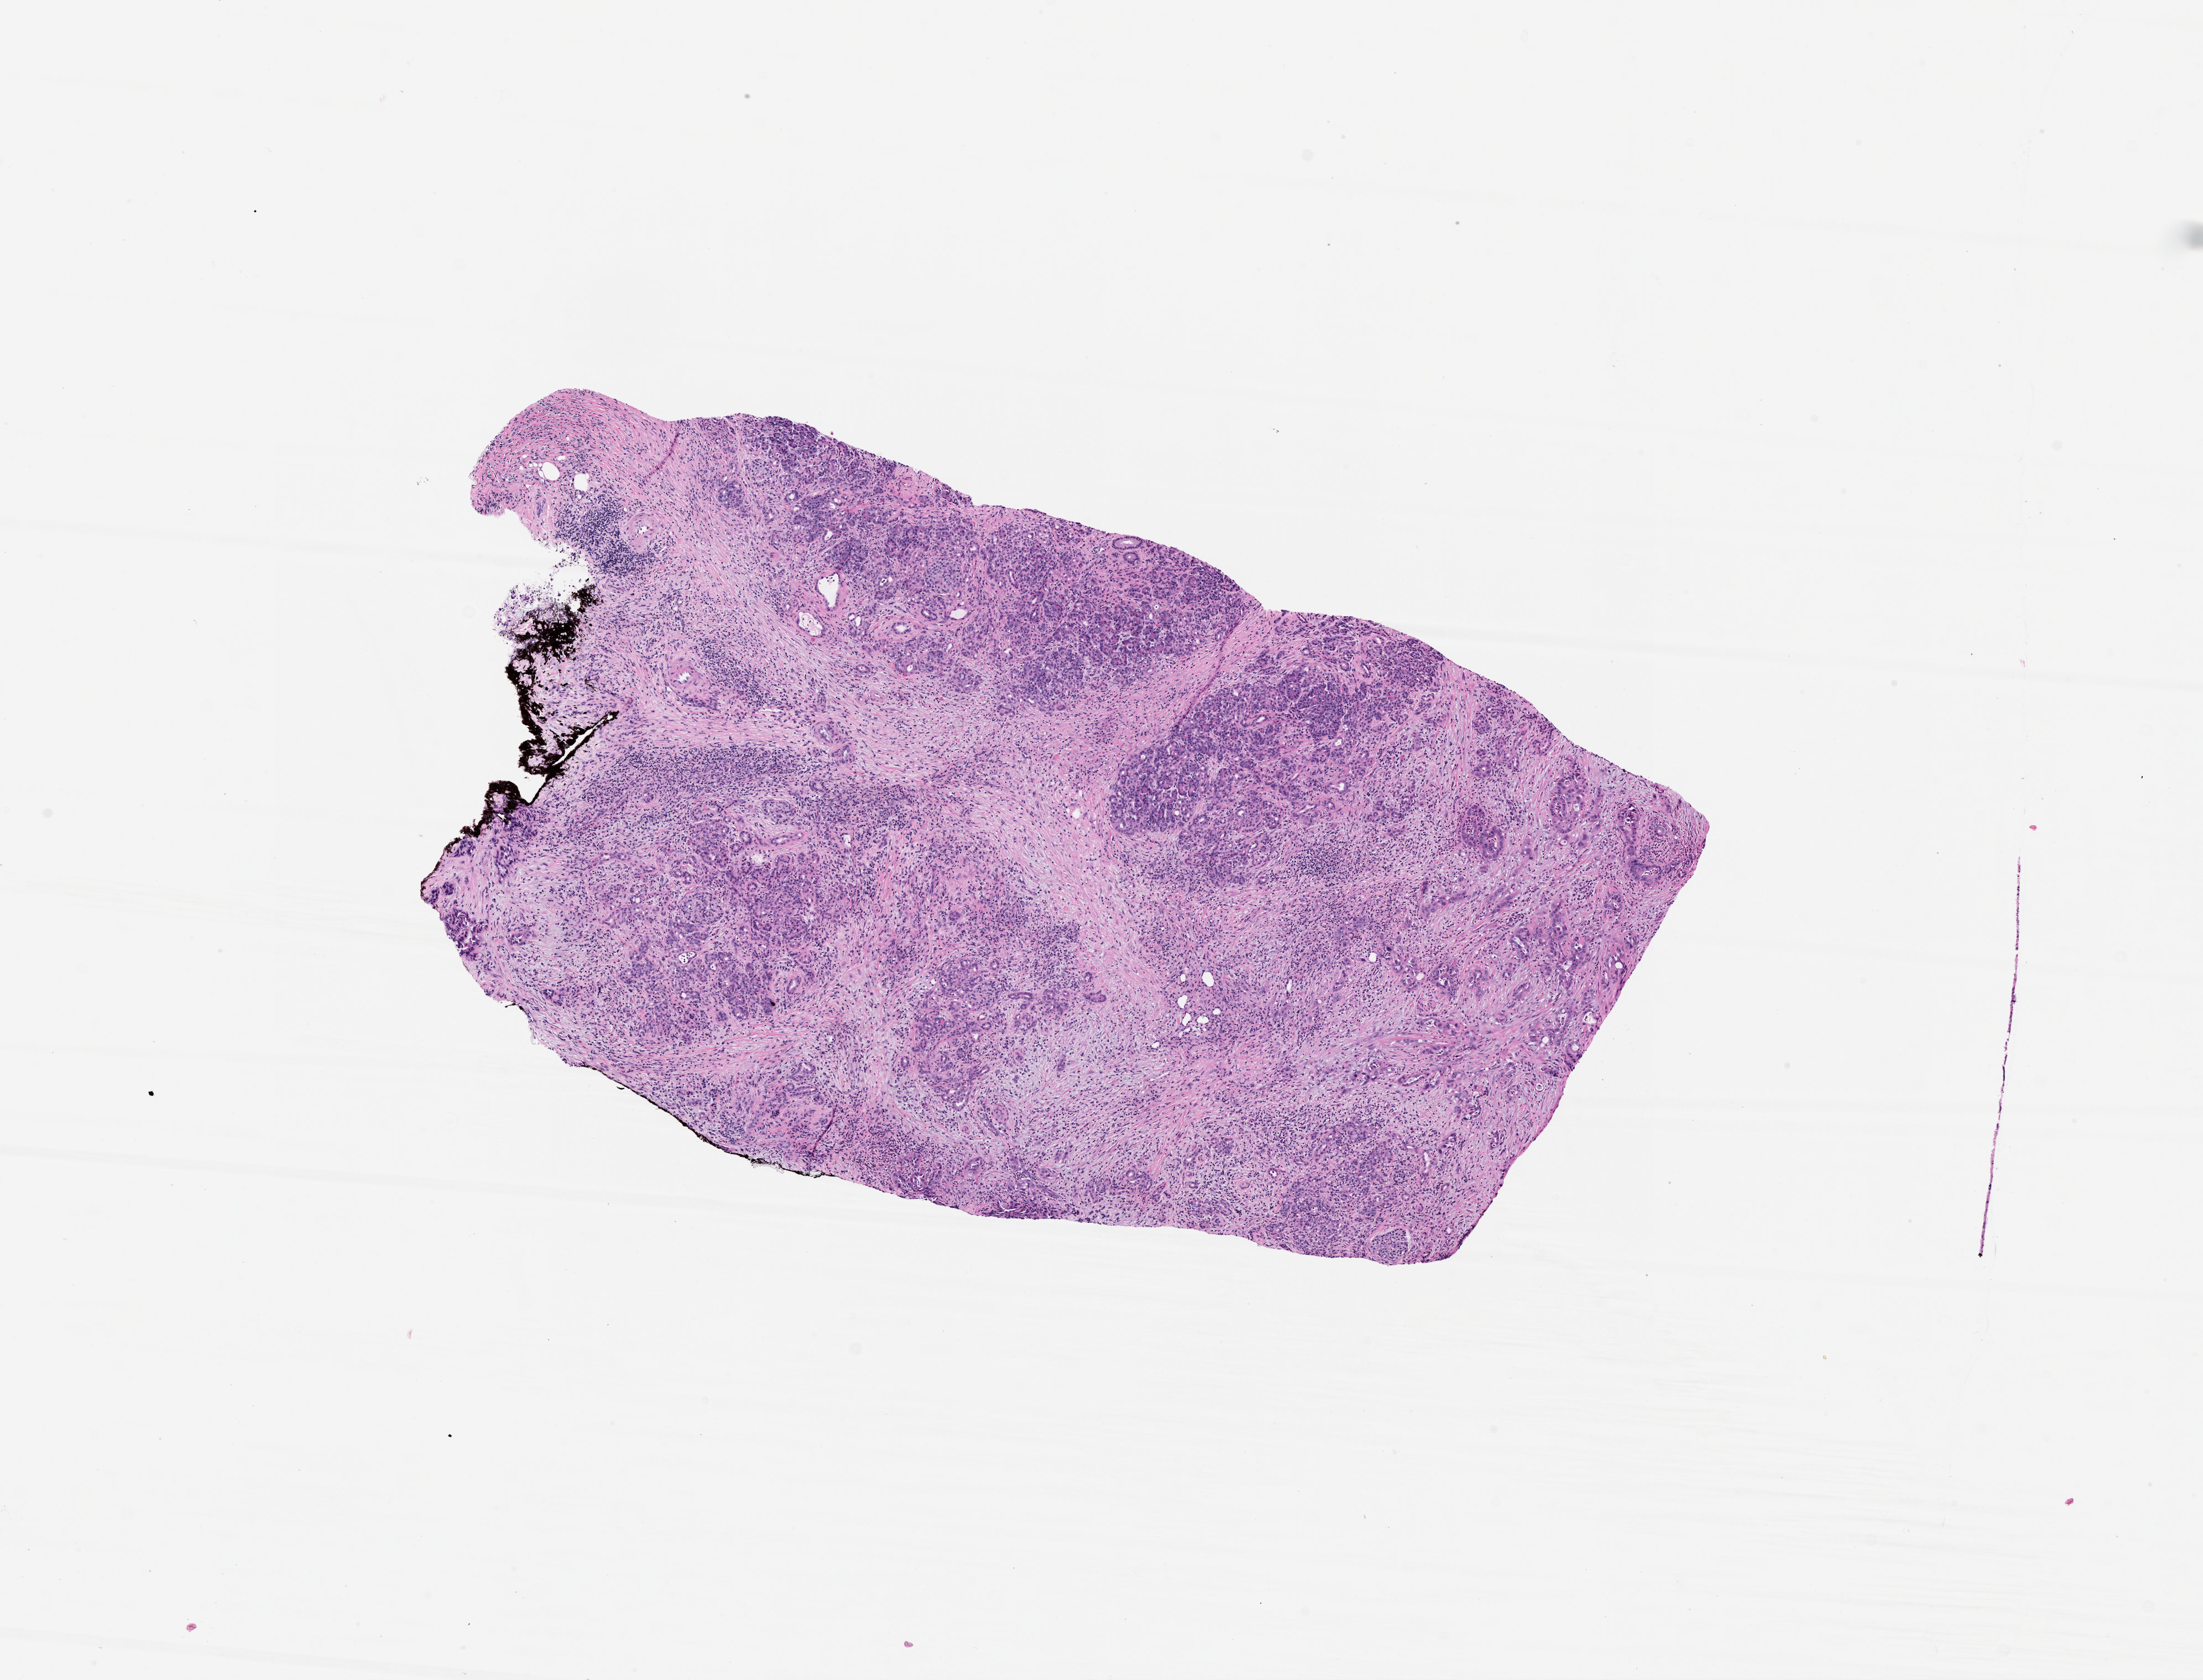
H&E whole-slide image — a low-resolution overview of the entire scanned area, about 8.0 x 6.1 mm; tumour tissue sample, sampled site: pancreas. 85-year-old female patient. Slide review estimates, as recorded: tumour nuclei 1%, necrosis 0%.
Diagnosis: Infiltrating duct carcinoma, NOS.